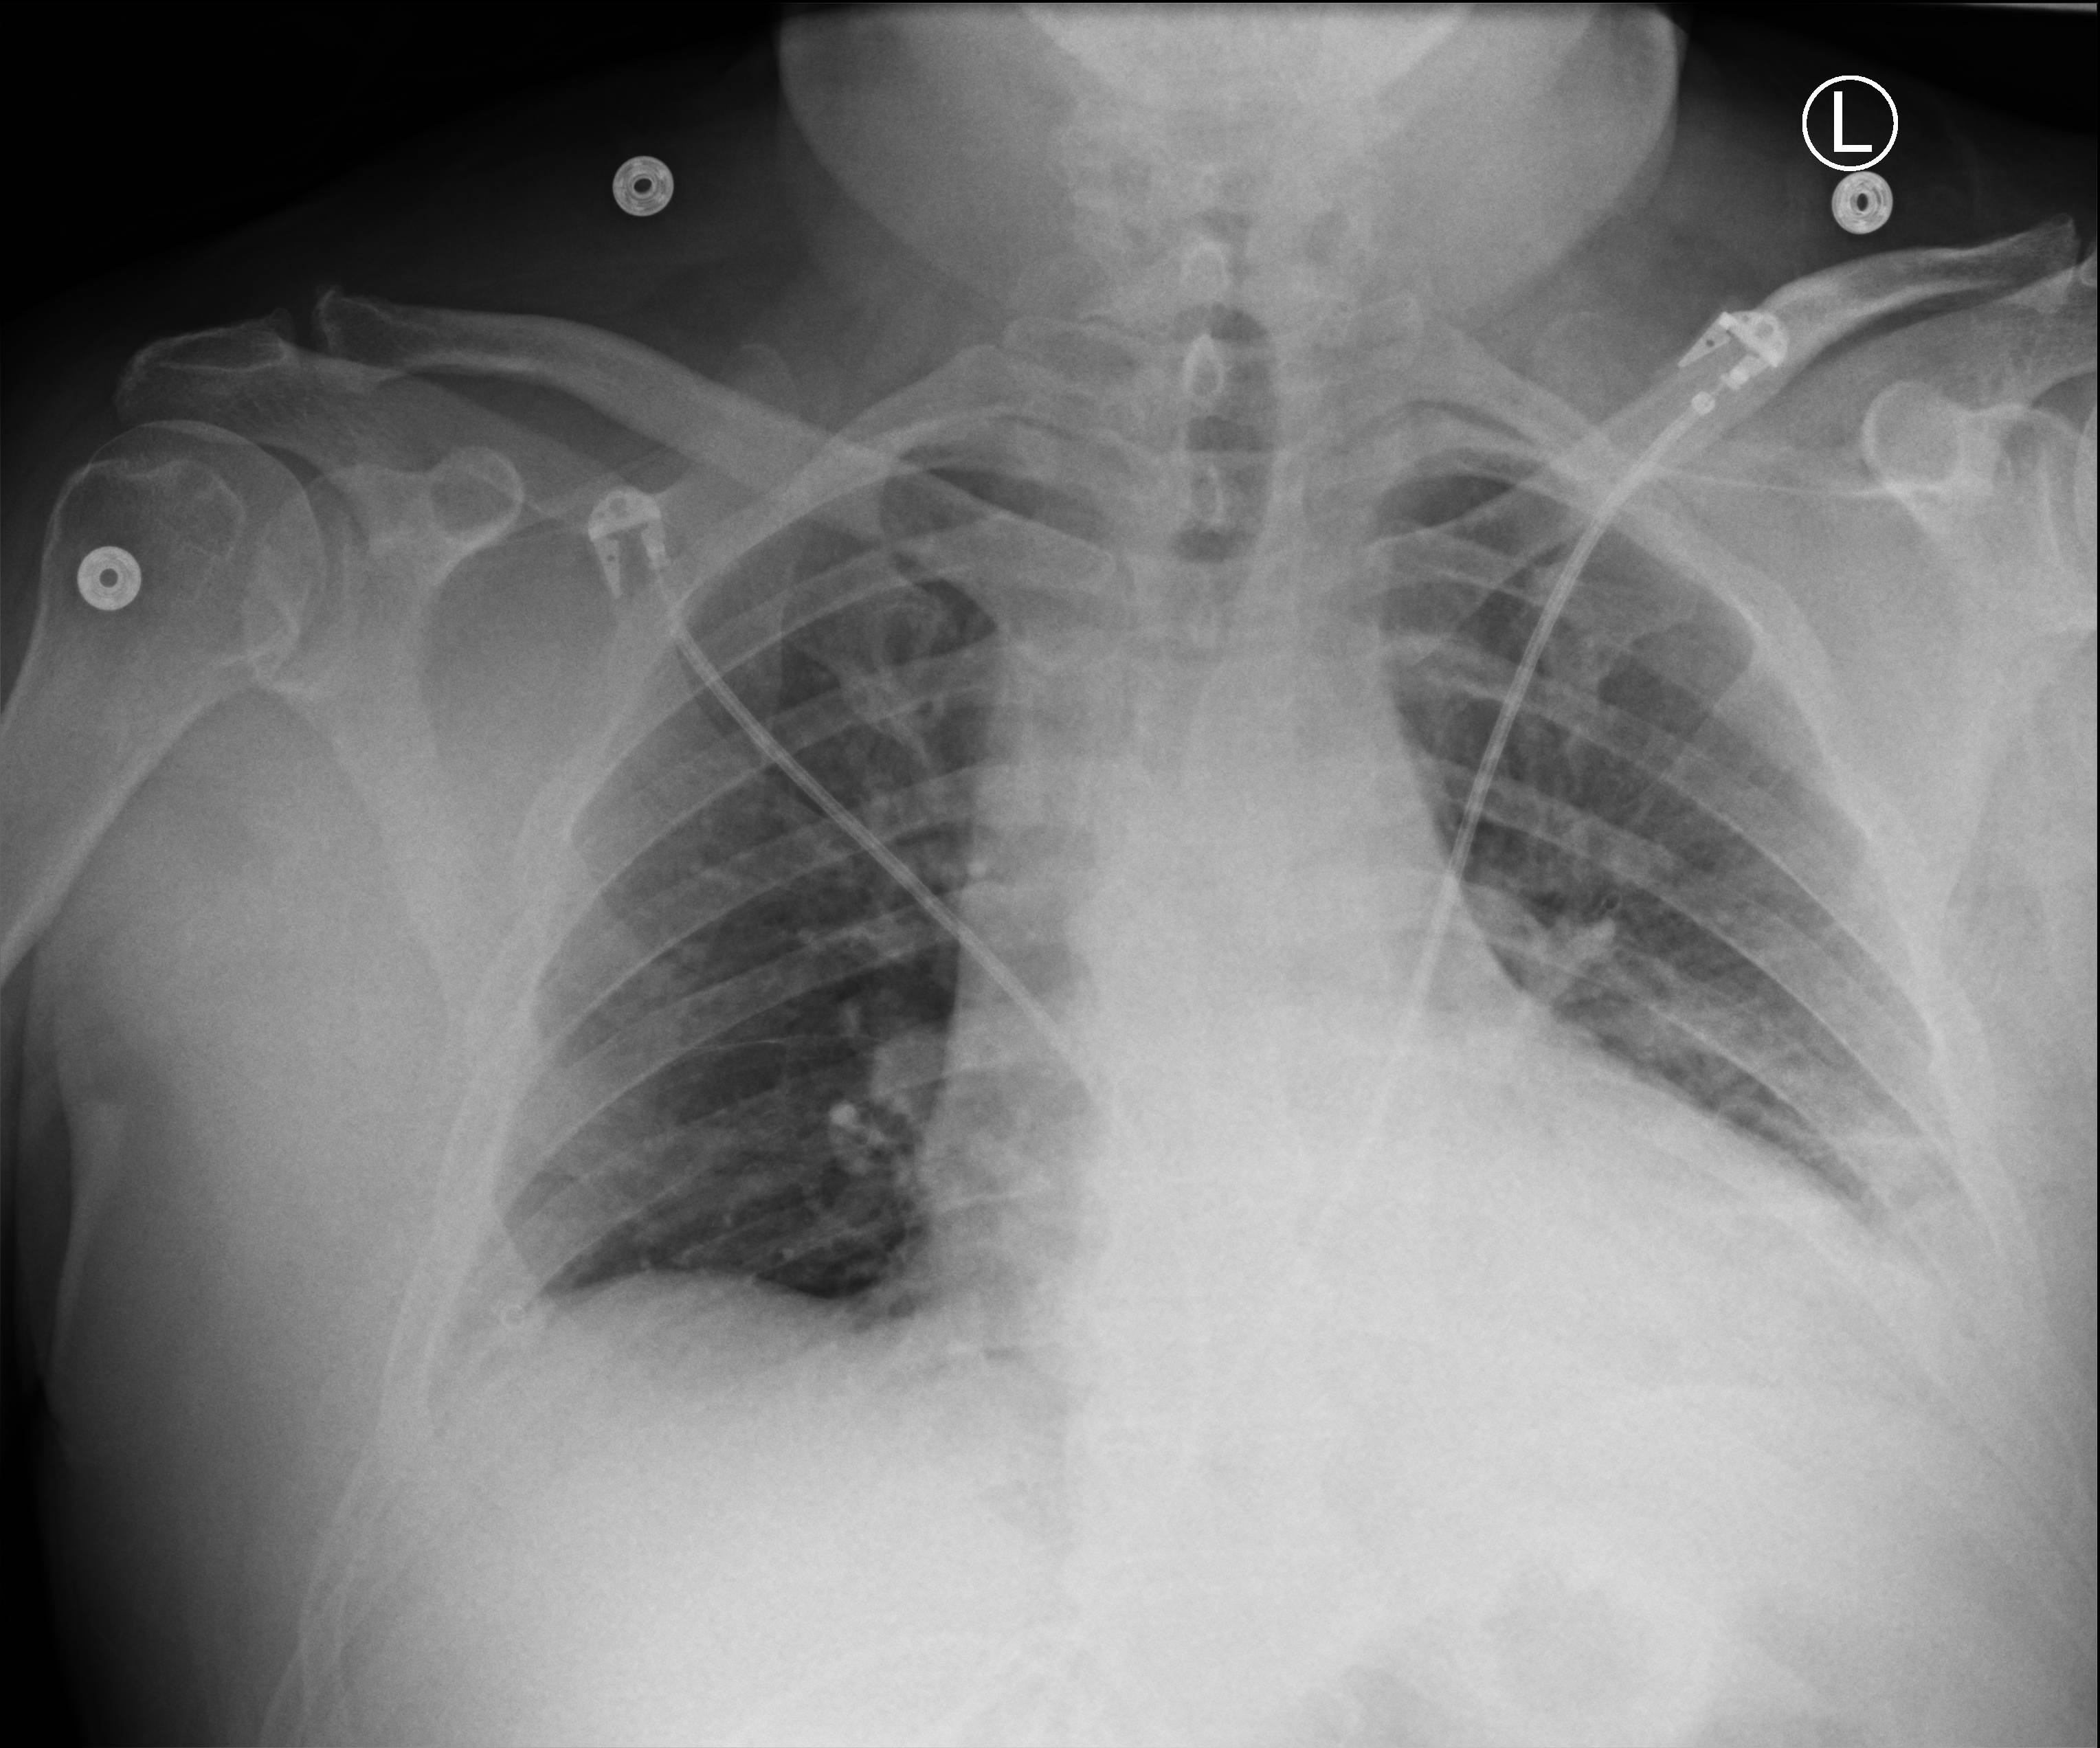
Bedside chest radiograph (computed radiography). Patient hospitalised with COVID-19; male, aged 18–59 years.
Admission-level facts for this patient (not findings on this image; timing relative to this image not recorded): mechanically ventilated during this hospital stay: no; admitted to intensive care during this hospital stay: no.